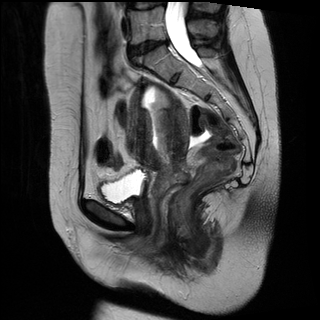
Pelvic MRI for cervical cancer, one sagittal slice. Slice 17 of 34 in the series (ordered by position). T2-weighted. 1.5 T. TE 89 ms, TR 3320 ms. 4 mm slice thickness. 320 × 320 image matrix, field of view 260 × 260 mm. Female patient, age 49 years.
Annotated regions visible in this slice (outlined manually by an expert reader):
- uterus and cervix: bounding box (x1, y1, x2, y2) in pixels: (127, 78, 191, 200)